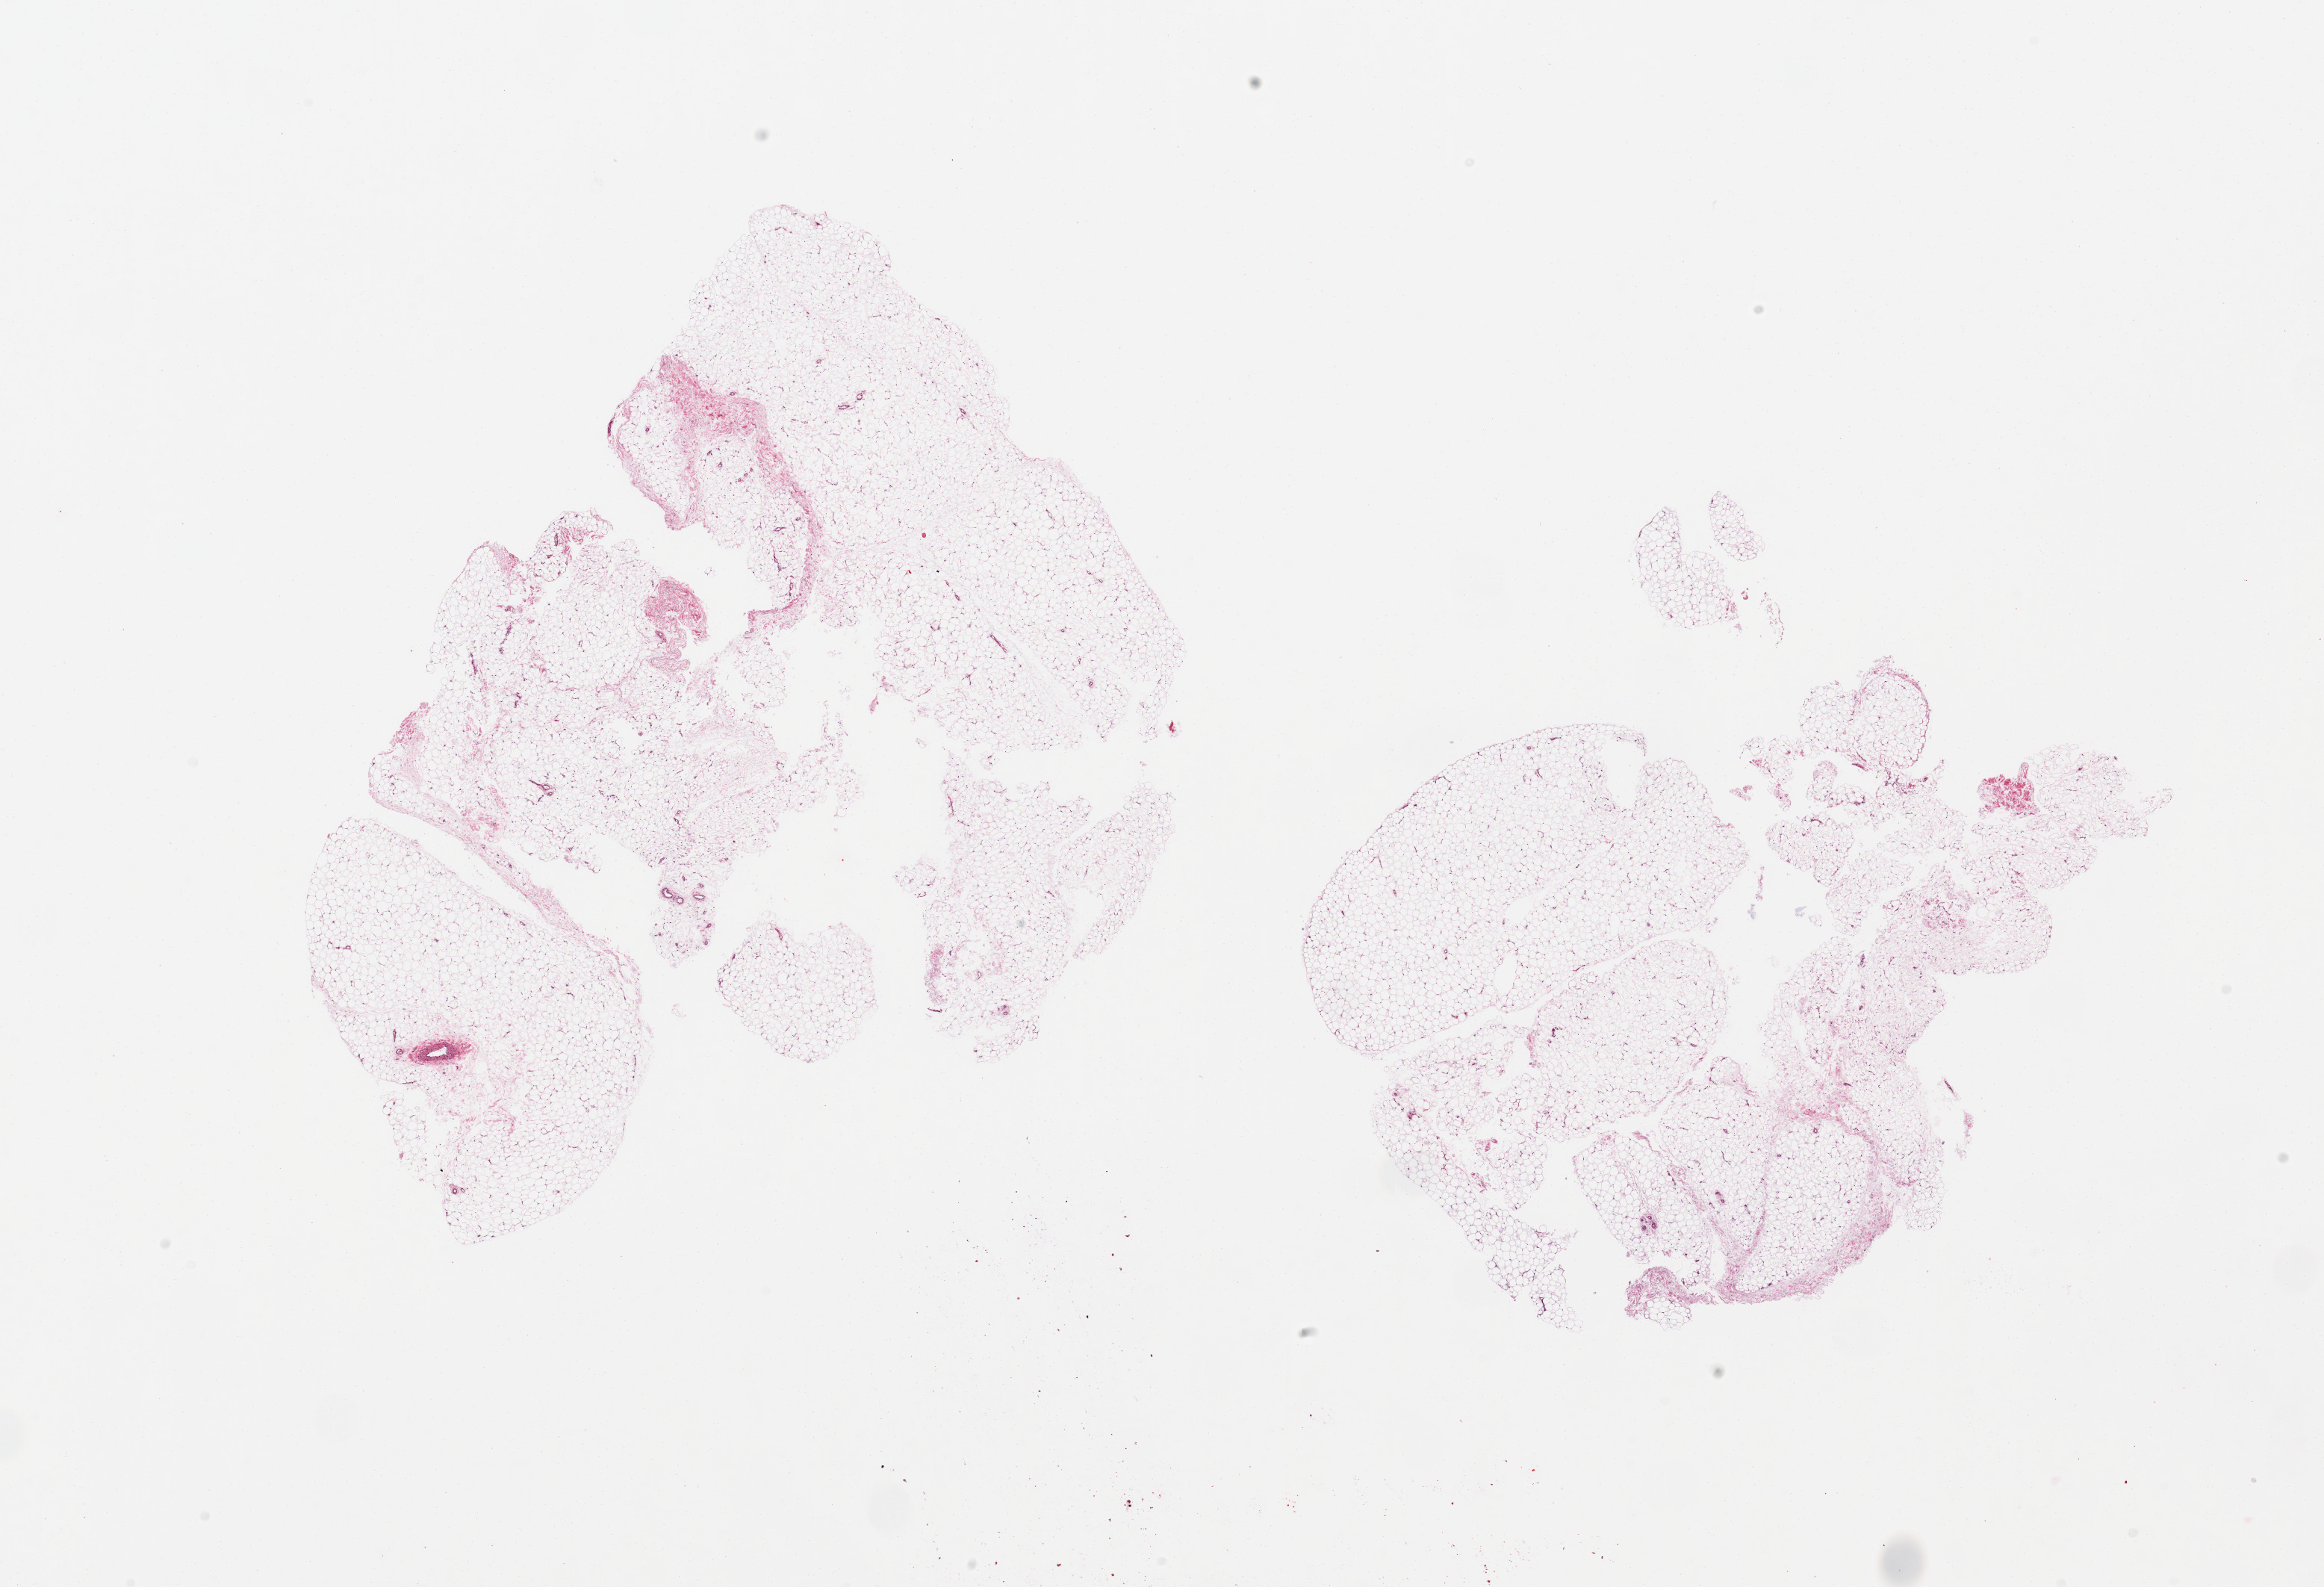
Digitized haematoxylin and eosin-stained section, brightfield, shown as a low-resolution overview of the whole scanned area (about 24.6 x 16.8 mm, slide scanned at 20x). PAXgene-fixed paraffin-embedded (PFPE) section. Sampled site (target tissue): adipose tissue. Donor tissue sample. Donor sex: male.
* reviewer comment on this tissue sample: 2 pieces; mature fat